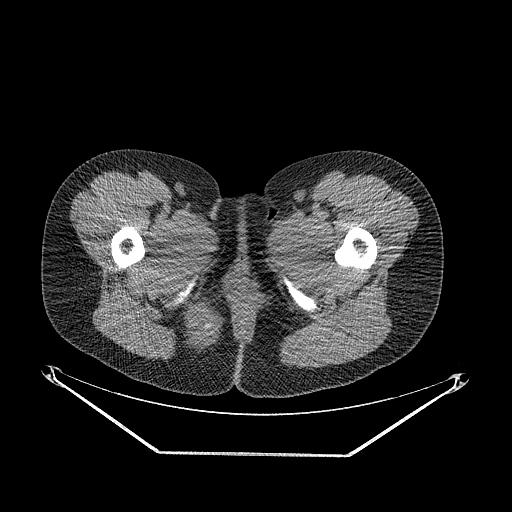
CT of an extremity soft-tissue mass (from a PET/CT study), one axial slice; position 30 of 267 along the scan axis; reconstruction kernel STANDARD; 120 kVp; soft-tissue window (W 400 / L 40 HU); 512 × 512 image matrix, field of view 500 × 500 mm. Female patient. From the clinical record (not read from this slice): histological type: epithelioid sarcoma; grade: intermediate; site of the primary tumour: right buttock.
Annotated regions visible in this slice (expert contour drawn on MRI and transferred to this co-registered scan by the dataset authors):
- gross tumour volume including surrounding oedema: bounding box [x1, y1, x2, y2] px = [174, 297, 225, 355]
- gross tumour volume (mass): [178, 306, 222, 350]